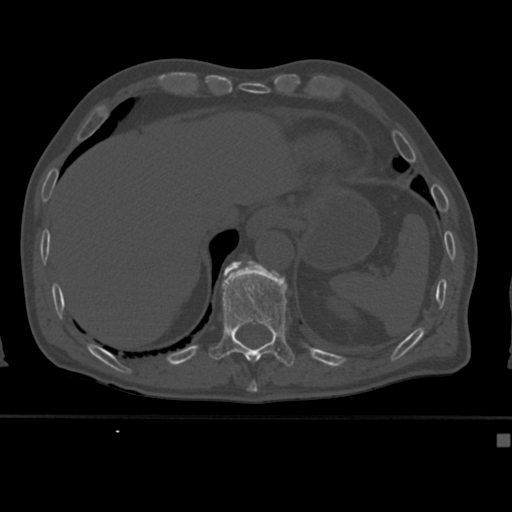
CT including the spine, one axial slice; slice 211 of 430 in the series (ordered by position); reconstruction kernel Br40s; 120 kVp; bone window (W 1800 / L 400 HU); 512 × 512 image matrix, field of view 337 × 337 mm. Male patient, age 64 years. From the clinical record (not read from this slice): primary cancer: uterus.
Annotated regions visible in this slice (semi-automatic segmentation, software-assisted and operator-edited):
- T11 vertebra: box from (x=208, y=265) to (x=295, y=367) px
- T12 vertebra: (x=224, y=261)–(x=240, y=271)